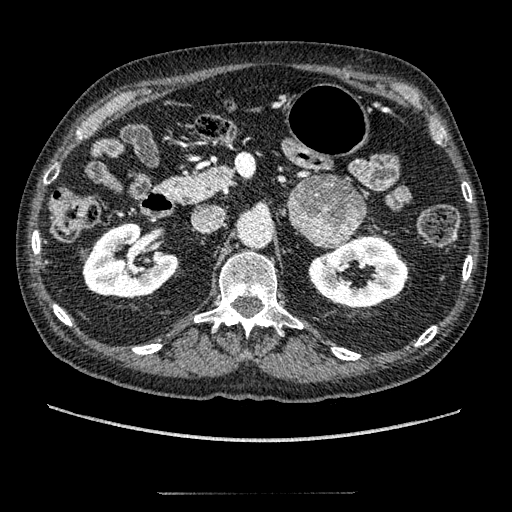
Contrast-enhanced abdominal CT, one axial slice; position 112 of 274 along the scan axis; 120 kVp; soft-tissue window (W 400 / L 40 HU); 1.25 mm slice thickness; 512 × 512 image matrix, field of view 381 × 381 mm. Male patient, age 69 years. From the clinical record (not read from this slice): diagnosis: adrenocortical carcinoma; tumour side: left adrenal; tumour size at pathology: 6.1 cm.
Structures marked on this image (semi-automatic segmentation, software-assisted and operator-edited):
- mass: bounding box (x1, y1, x2, y2) in pixels: (288, 175, 366, 247)